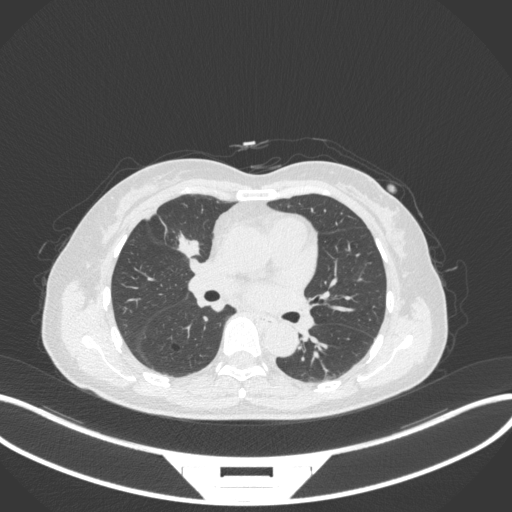
Chest CT, one axial slice; position 163 of 282 along the scan axis; lung window (W 1500 / L -600 HU); 1 mm slice thickness; 512 × 512 image matrix, field of view 400 × 400 mm. Female patient, age 51 years. Case-level facts recorded for this patient, not image findings: clinical TNM (as recorded): T1c N0 M0; histopathological grade: G2.
Annotated regions visible in this slice (rectangle marked by the reading radiologist):
- lung tumour (recorded histology: adenocarcinoma): bounding box <172,227,206,263> (left, top, right, bottom; pixels)